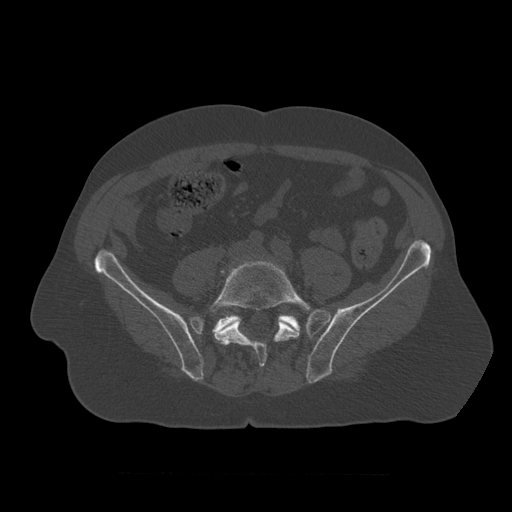
CT including the spine, one axial slice. Position 252 of 450 along the scan axis. 120 kVp. Bone window (W 1800 / L 400 HU). 1.25 mm slice thickness. 512 × 512 image matrix, field of view 405 × 405 mm. Patient age 75 years. From the clinical record (not read from this slice): primary cancer: prostate.
Outlined on this slice (semi-automatically segmented with operator editing):
- L5 vertebra: box from (x=210, y=261) to (x=317, y=367) px